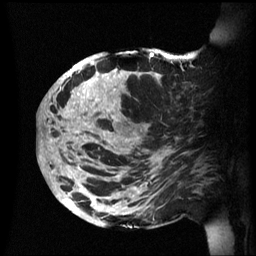
Breast MRI (dynamic contrast-enhanced), one sagittal slice; slice 27 of 60 in the series (ordered by position); dynamic contrast-enhanced series, image 2 of 3 at this slice position (ordered by acquisition); 1.5 T; TE 4.2 ms, TR 8.4 ms; 2.4 mm slice thickness; 256 × 256 image matrix, field of view 230 × 230 mm. Patient: female, 48 years.
Annotated regions visible in this slice (semi-automatic segmentation, software-assisted and operator-edited):
- analysis volume of interest (the breast-tissue region the enhancement analysis was run in; not a lesion): box from (x=42, y=48) to (x=202, y=229) px
- tumour enhancement mask (voxels above the 70 % enhancement threshold inside the analysis volume of interest): (x=42, y=53)–(x=169, y=226)